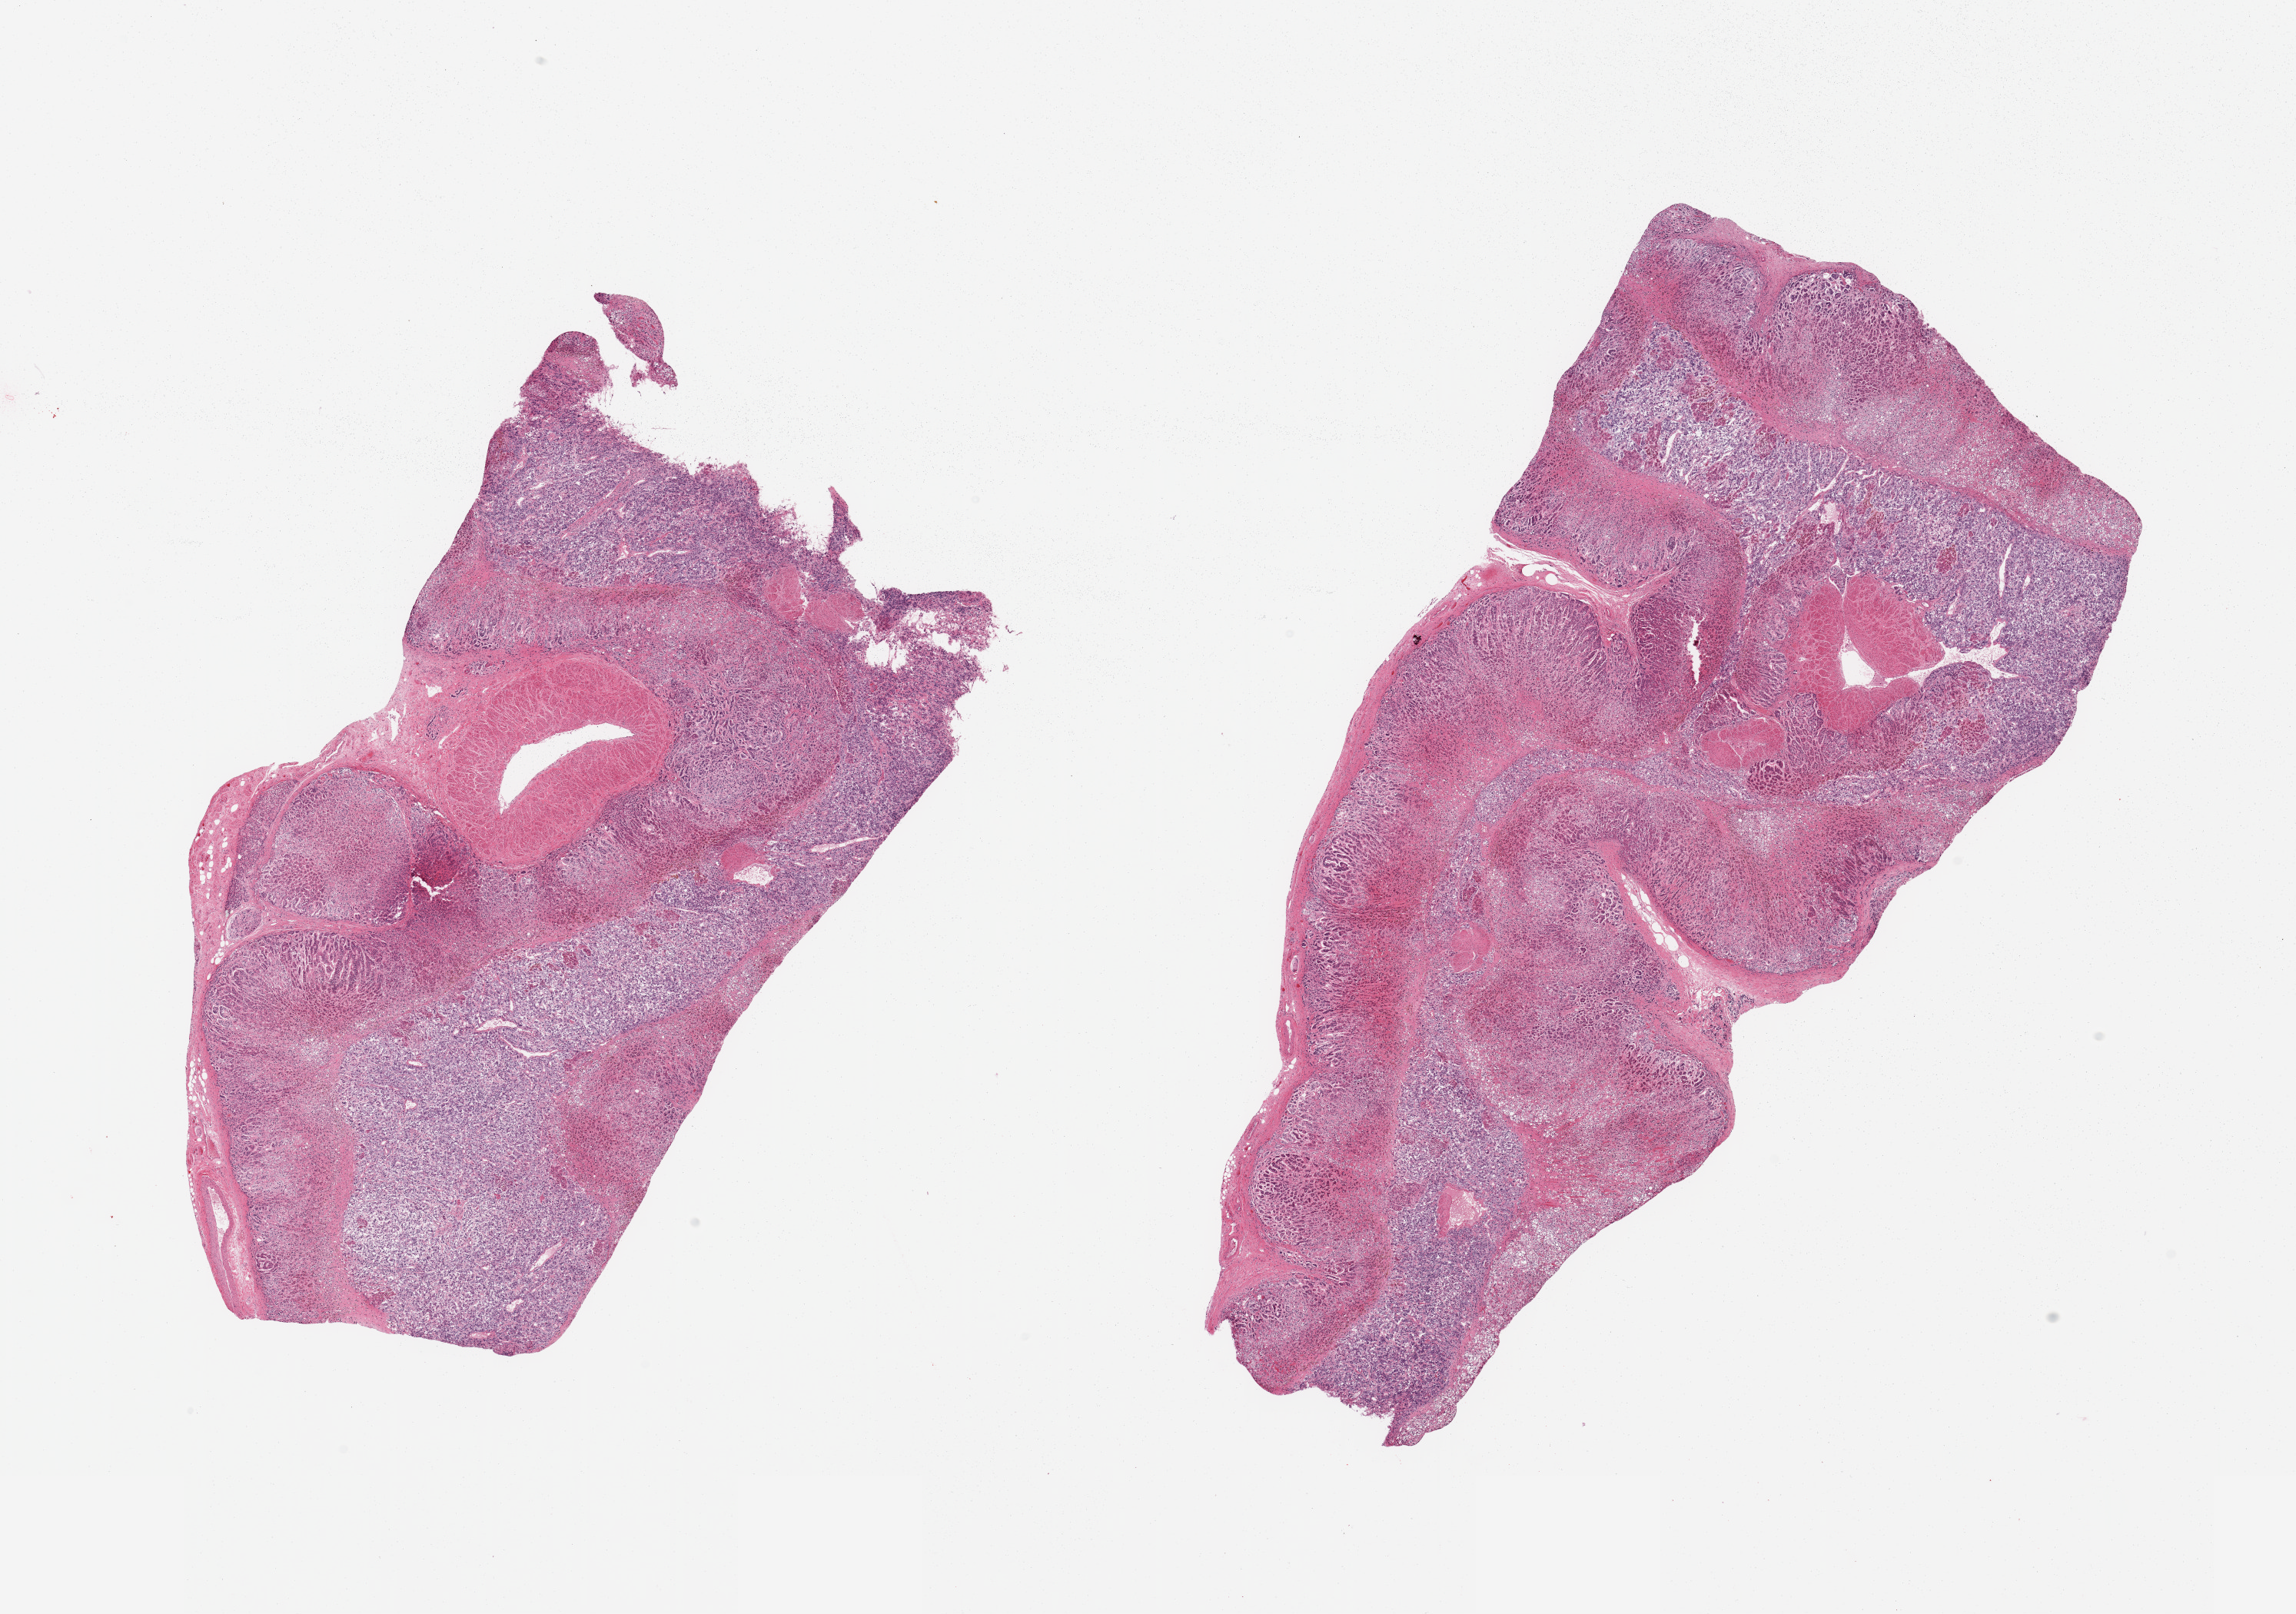
Hematoxylin and eosin (H&E) whole-slide image — shown as a low-resolution overview of the whole scanned area (about 23.6 x 16.6 mm); PAXgene-fixed paraffin-embedded (PFPE) section; section of adrenal gland (target tissue); donor tissue sample.
Reviewer comment on this tissue sample: 2 pieces; well dissected.